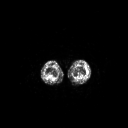
FDG PET of an extremity soft-tissue mass (from a PET/CT study), one axial slice; 3.27 mm slice thickness; 128 × 128 image matrix, field of view 700 × 700 mm. Patient: female, 16 years. From the clinical record (not read from this slice): histological type: spindle cell suggestive of biphasic synovial sarcoma; grade: intermediate; site of the primary tumour: left knee.
Annotated regions visible in this slice (expert contour drawn on MRI and transferred to this co-registered scan by the dataset authors):
- gross tumour volume including surrounding oedema: bounding box (x1, y1, x2, y2) in pixels: (86, 69, 88, 71)